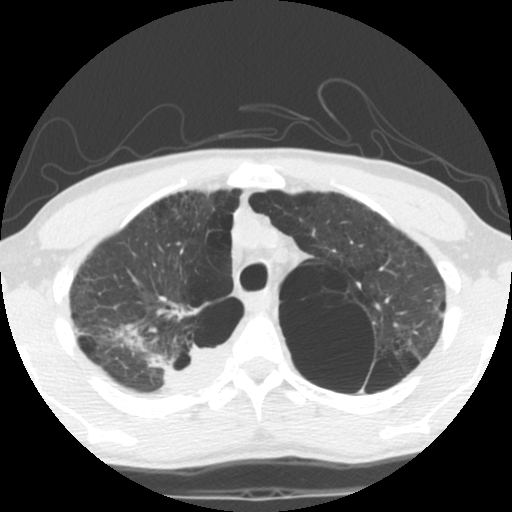
Low-dose screening chest CT, axial slice. Second screening round (one year after baseline). Lung window (W 1500 / L -600 HU). Standard (soft-tissue) reconstruction kernel (STANDARD). 512 × 512 image matrix. Male, age 62 years at enrolment. Current smoker at enrolment.
• Expert reader's lesion annotation, bounding box [x1, y1, x2, y2] px = [125, 322, 217, 396].
• The exam's reader record, not a measurement of the box and not confirmed to be the same lesion: non-calcified nodule or mass ≥4 mm, 35 × 25 mm, soft tissue attenuation.
• Official screen result: positive, other.
• Participant outcome: lung cancer diagnosed 14 days after this screen — non-small cell carcinoma, right upper lobe, poorly differentiated (G3), stage IA (AJCC 6th edition), 70 mm at pathology.